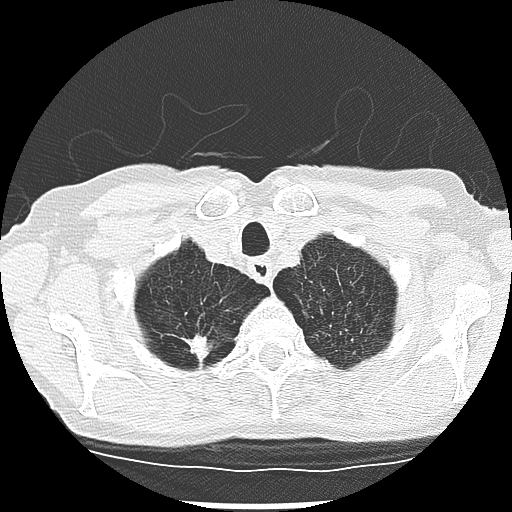
Low-dose screening chest CT, one axial slice; position 242 of 265 along the scan axis; reconstruction kernel LUNG; lung window (W 1500 / L -600 HU); 2.5 mm slice thickness; 512 × 512 image matrix, field of view 300 × 300 mm.
Annotated regions visible in this slice (manually delineated by an expert):
- lesion 2 (tumor, upper lobe of right lung): bounding box (x1, y1, x2, y2) in pixels: (187, 335, 210, 361)